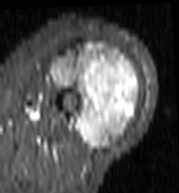
MRI of an extremity soft-tissue mass, one axial slice; position 51 of 103 along the scan axis; STIR; MR volume resampled by the dataset authors to the PET/CT grid (not the native acquisition matrix); 179 × 193 image matrix. Female patient. Case-level facts recorded for this patient, not image findings: histological type: undifferentiated – high grade; grade: high; site of the primary tumour: left thigh.
Annotated regions visible in this slice (expert contour drawn on MRI and transferred to this co-registered scan by the dataset authors):
- gross tumour volume including surrounding oedema: bounding box [x1, y1, x2, y2] px = [50, 44, 140, 150]
- gross tumour volume (mass): [52, 44, 140, 150]